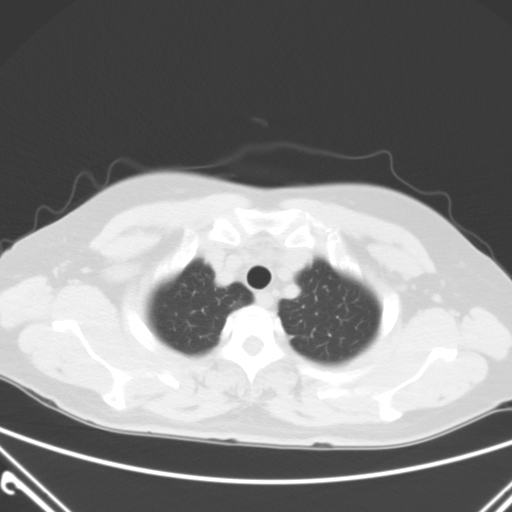
Chest CT, one axial slice; position 50 of 60 along the scan axis; 120 kVp; lung window (W 1500 / L -600 HU); 5 mm slice thickness; 512 × 512 image matrix, field of view 350 × 350 mm. Patient: female, 54 years. From the clinical record (not read from this slice): clinical TNM (as recorded): T1a N0 M0.
Annotated regions visible in this slice (bounding box drawn by a radiologist):
- lung tumour (recorded histology: adenocarcinoma): bounding box (x1, y1, x2, y2) in pixels: (226, 294, 249, 312)